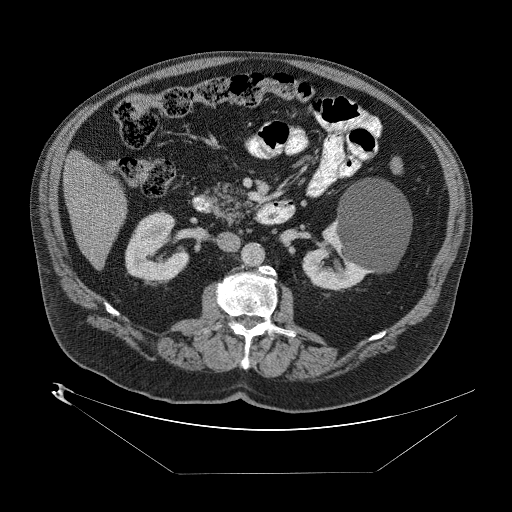
Contrast-enhanced abdominal CT (liver protocol), one axial slice. Slice 17 of 89 in the series (ordered by position). Reconstruction kernel STANDARD. One of 2 acquisitions stored at this slice position. Soft-tissue window (W 400 / L 40 HU). 512 × 512 image matrix. Case-level facts recorded for this patient, not image findings: diagnosis: hepatocellular carcinoma (patient treated with transarterial chemoembolisation; whether this scan precedes or follows treatment is not stated here); TNM stage (as recorded): Stage-II; Child-Pugh class: B; tumour differentiation: moderately differentiated; tumour nodularity: multinodular.
Outlined on this slice (semi-automatically segmented with operator editing):
- abdominal aorta: box from (x=244, y=244) to (x=265, y=266) px
- liver parenchyma outside the tumour (the mass and vessels are separate outlines, so this box may not span the whole liver): (x=62, y=144)–(x=126, y=264)